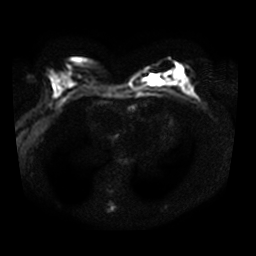
Breast MRI, one axial slice; position 18 of 34 along the scan axis; diffusion-weighted series; image 2 of 4 stored at this slice position (different b-values; order by instance number); 3 T; 256 × 256 image matrix, field of view 340 × 340 mm. Female patient.
Outlined on this slice (expert manual segmentation):
- tumour on diffusion-weighted imaging: box from (x=149, y=74) to (x=162, y=85) px